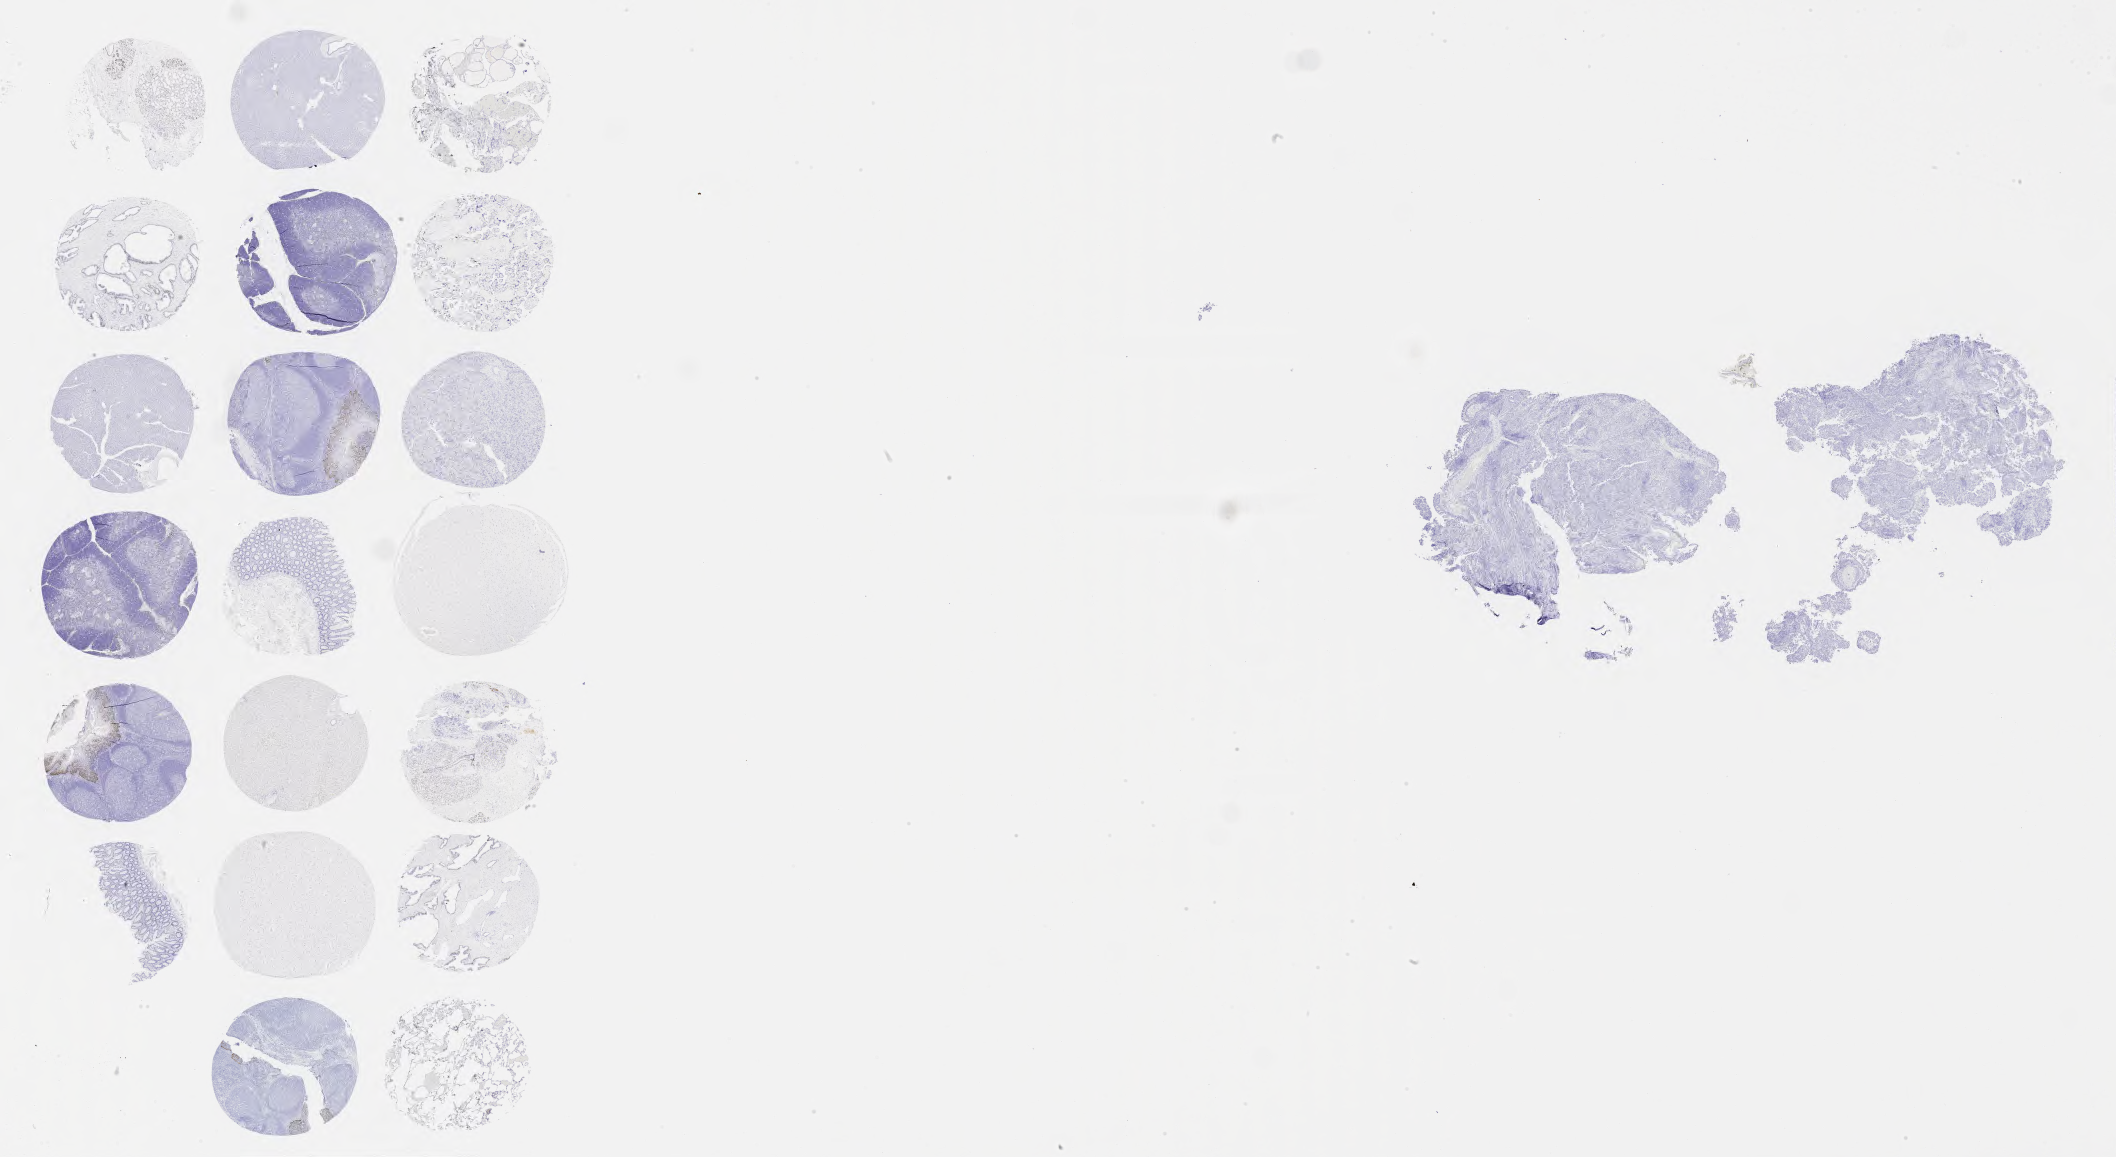
Whole-slide image, immunohistochemical stain for p40, low-resolution overview of the scanned area, about 34.2 x 18.7 mm; specimen: tumor tissue; site: cervix. Patient female; age 65 years.
• histologic diagnosis: Squamous cell carcinoma, large cell, nonkeratinizing, NOS